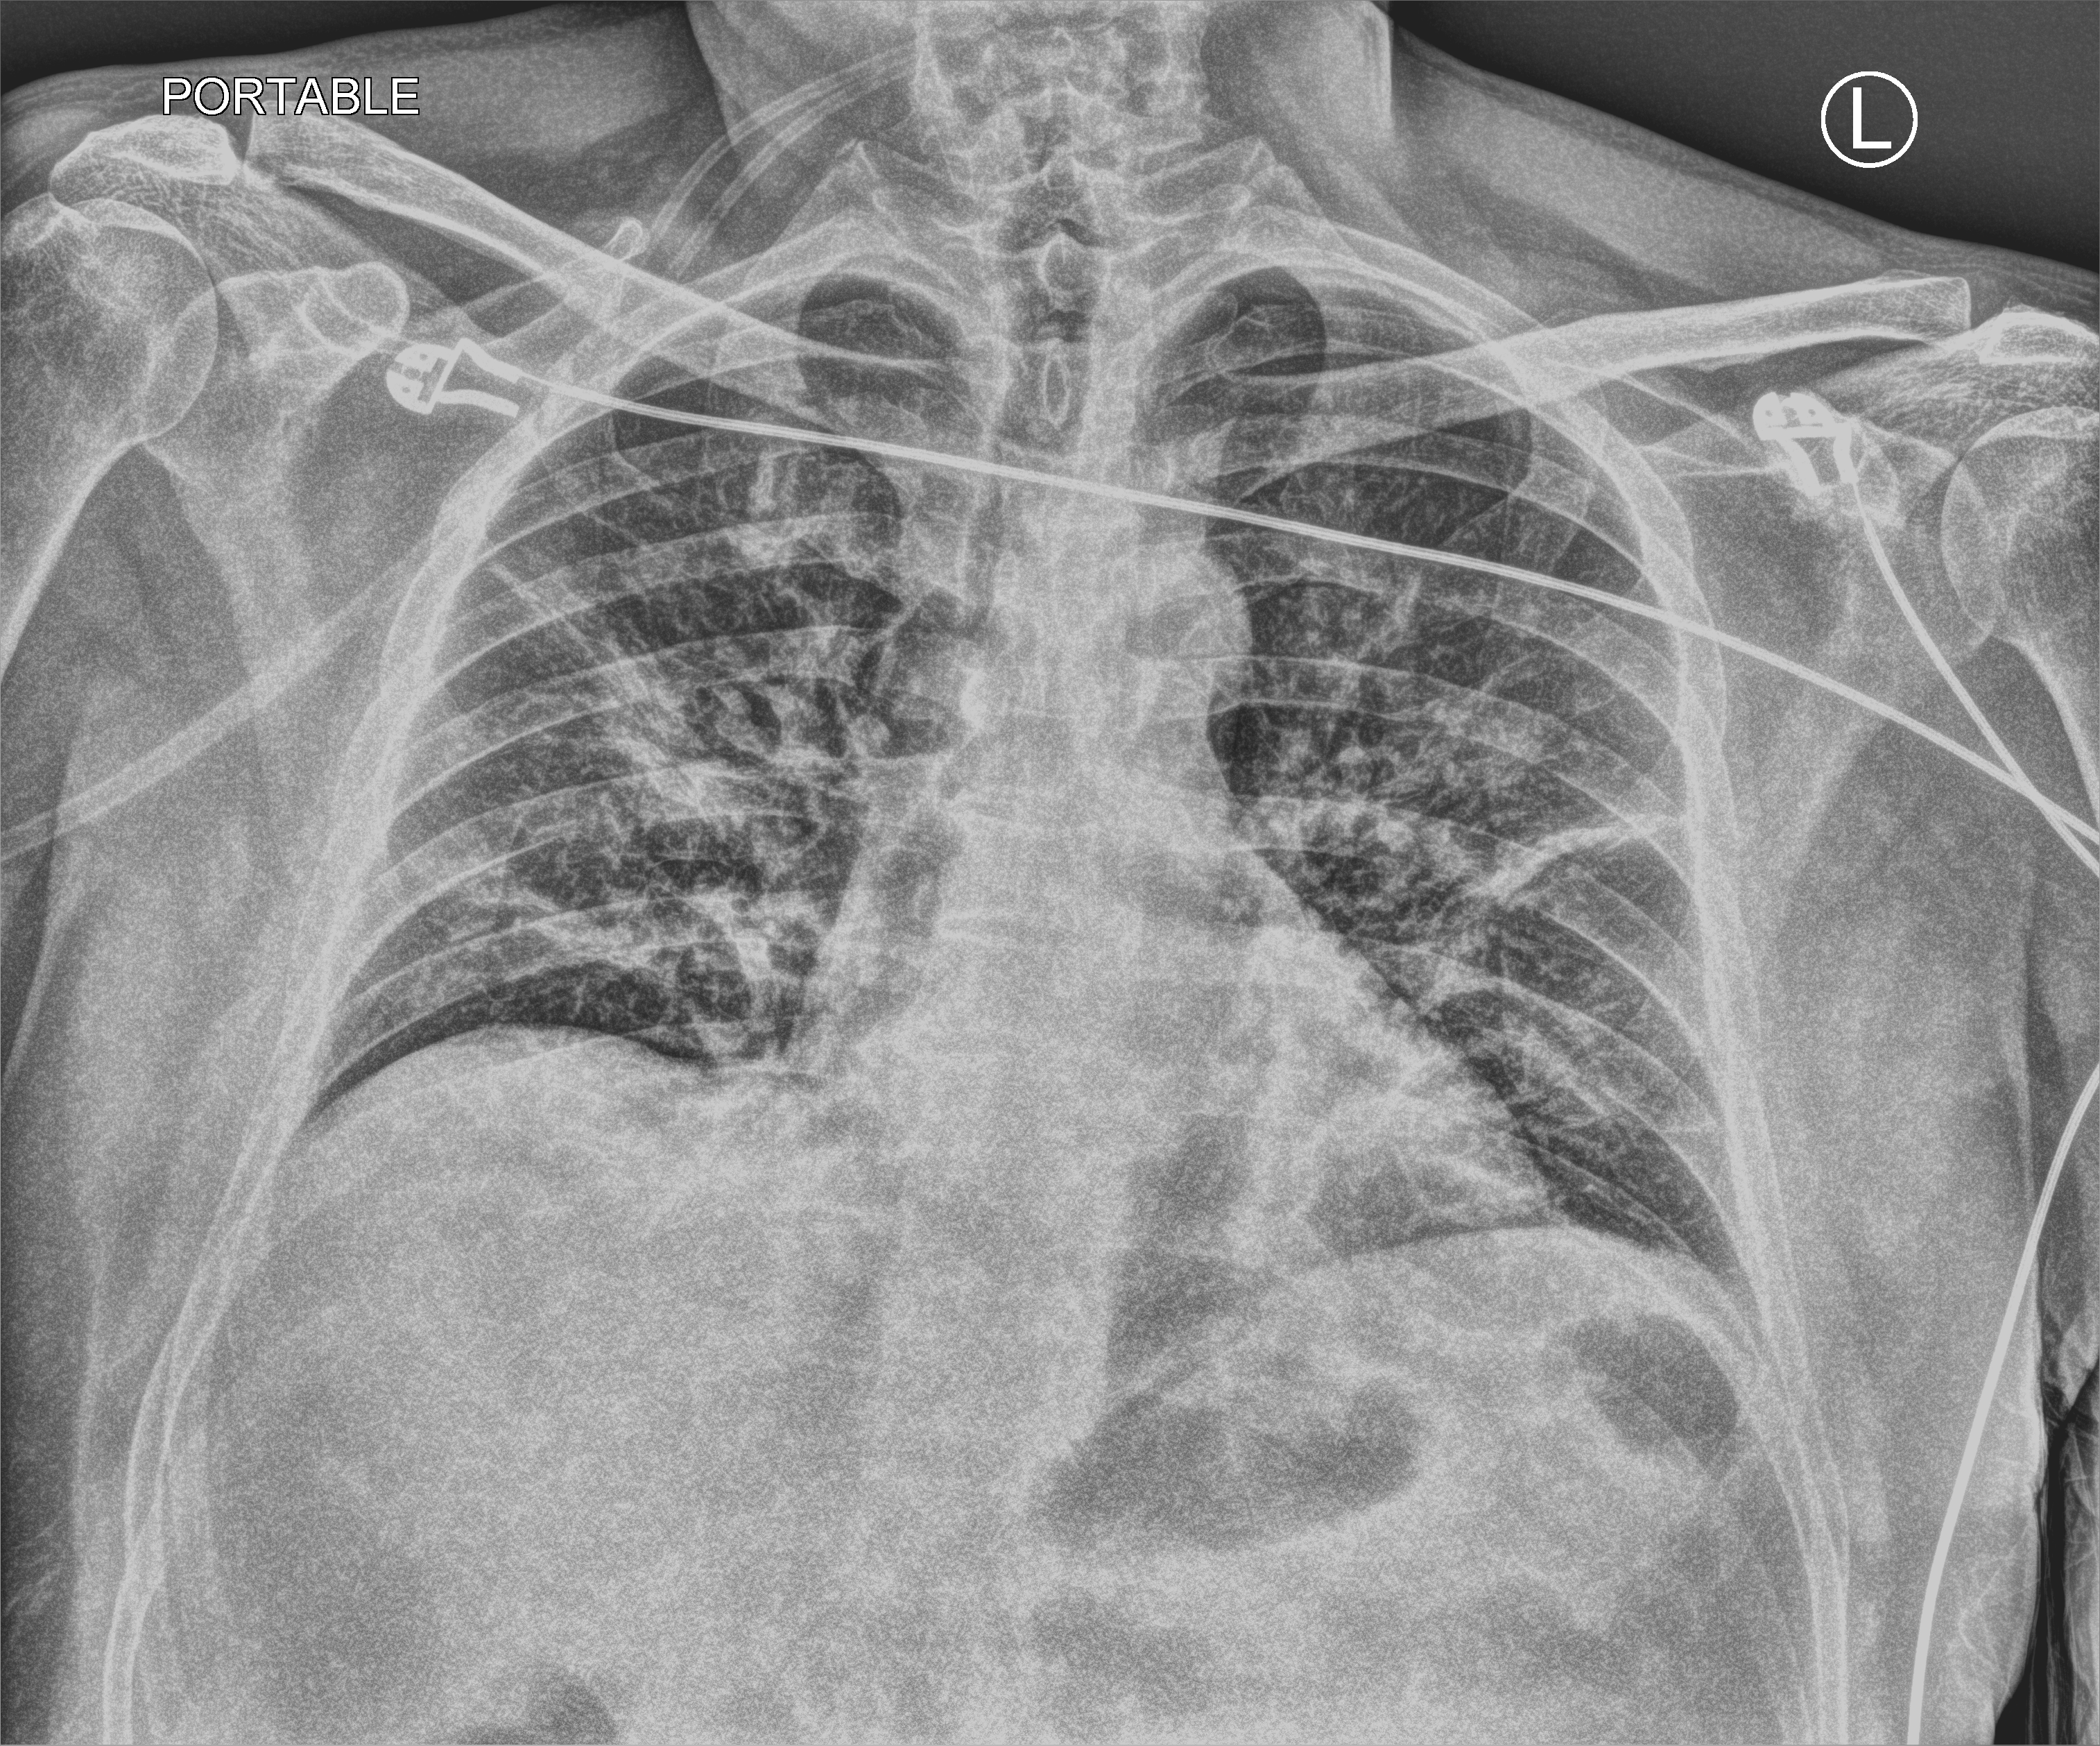
Bedside chest radiograph (computed radiography). Patient hospitalised with COVID-19; male, aged 18–59 years.
From the hospital-stay record, not from the radiograph (when in the stay this image was taken is not recorded):
- admitted to intensive care during this hospital stay: no
- length of hospital stay: 9 days
- mechanically ventilated during this hospital stay: no